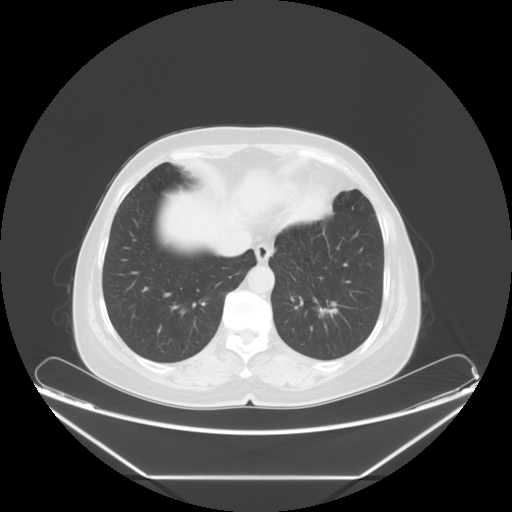
Chest CT, one axial slice; slice 17 of 61 in the series (ordered by position); lung window (W 1500 / L -600 HU); 5 mm slice thickness; 512 × 512 image matrix, field of view 451 × 451 mm. Female patient, age 63 years. Case-level facts recorded for this patient, not image findings: clinical TNM (as recorded): T1c N0 M0; histopathological grade: G2-3.
Annotated regions visible in this slice (rectangle marked by the reading radiologist):
- lung tumour (recorded histology: adenocarcinoma): bounding box [x1, y1, x2, y2] px = [311, 295, 339, 325]